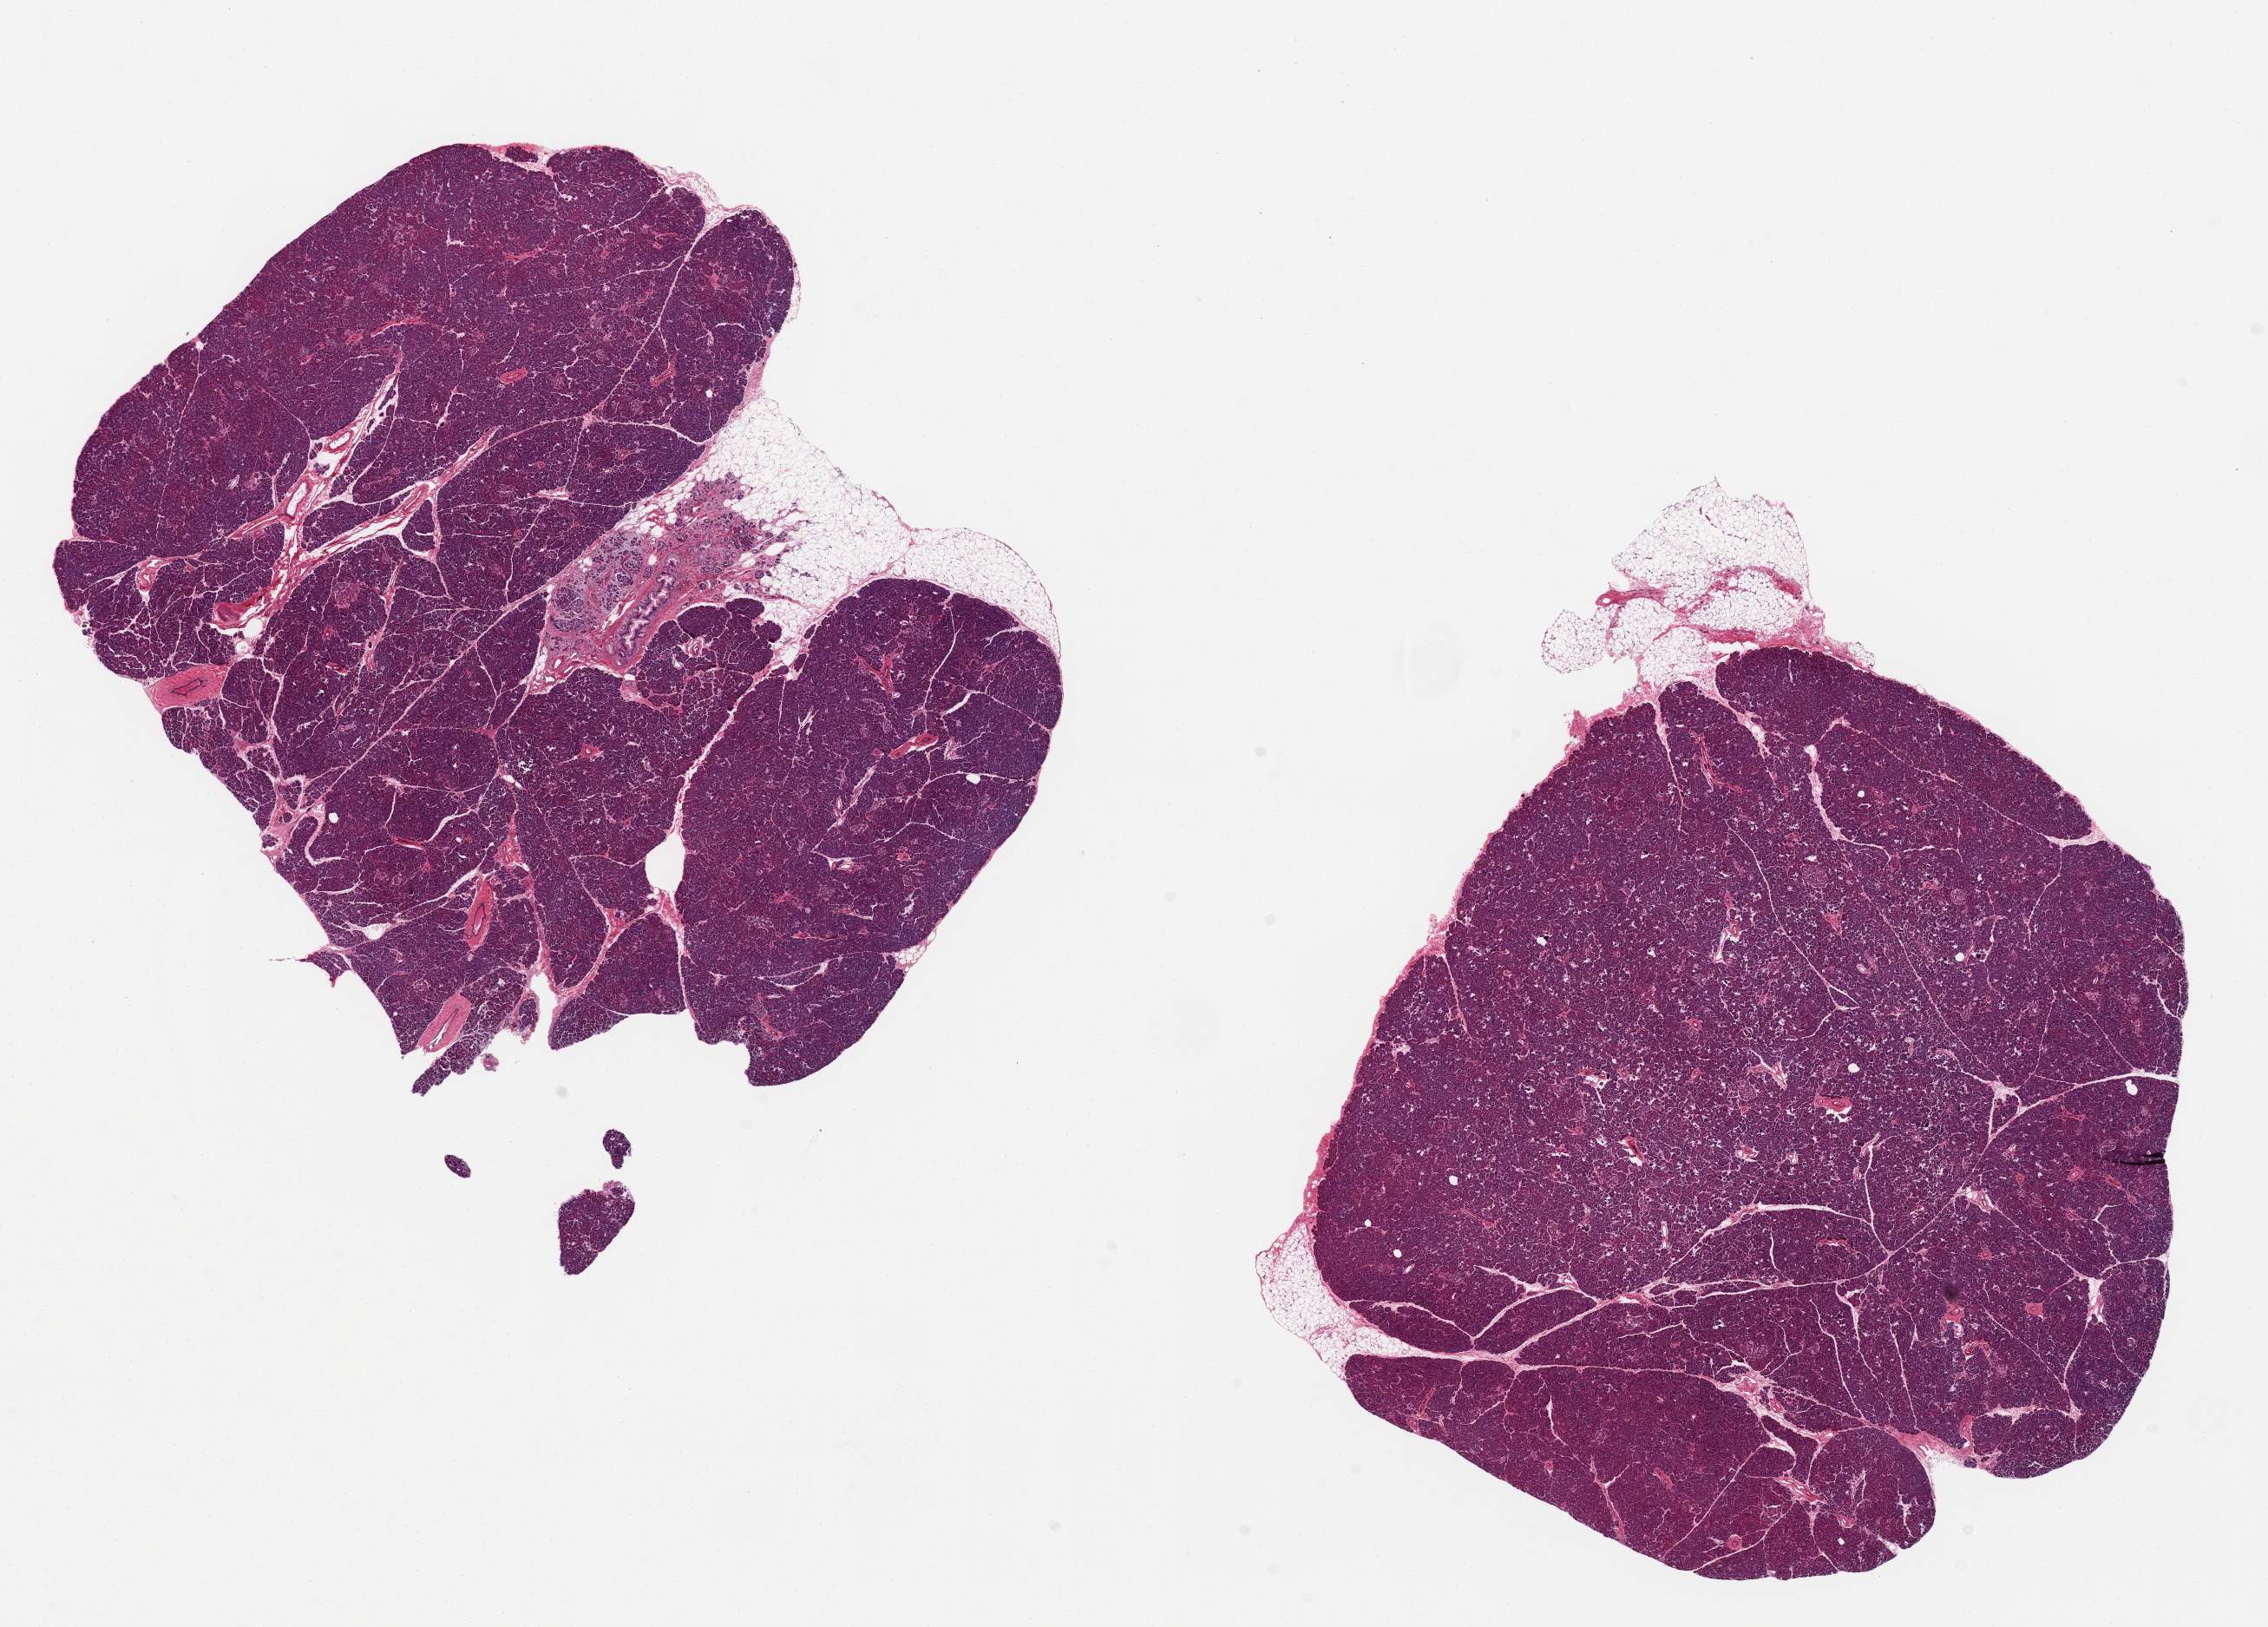
Digitized H&E-stained section, whole scanned area (about 20.7 x 14.8 mm) shown as a low-resolution overview. PAXgene-fixed paraffin-embedded (PFPE) section. Sampled site (target tissue): pancreas. Donor tissue sample. Donor: male.
- review note (as recorded): 2 pieces, ~9x7 & 8x8 mm; focal atrophic lobule; <10% adipose; islets ~150um appear normal